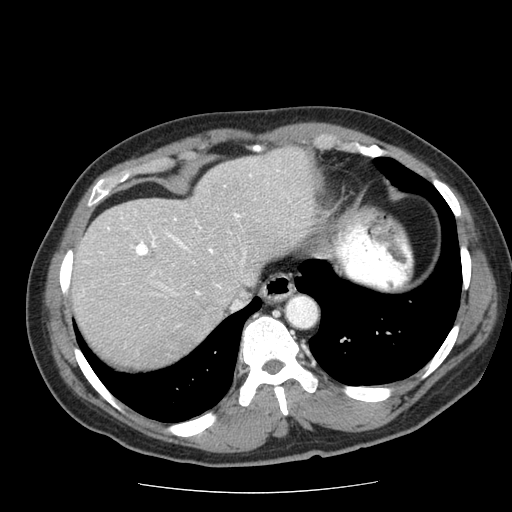
Contrast-enhanced abdominal CT (liver protocol), one axial slice. Position 54 of 85 along the scan axis. 120 kVp. Soft-tissue window (W 400 / L 40 HU). 512 × 512 image matrix. From the clinical record (not read from this slice): diagnosis: hepatocellular carcinoma (patient treated with transarterial chemoembolisation; whether this scan precedes or follows treatment is not stated here); TNM stage (as recorded): Stage-IIIA; Child-Pugh class: A; tumour differentiation: well differentiated; tumour nodularity: multinodular.
Outlined on this slice (semi-automatic segmentation, software-assisted and operator-edited):
- liver parenchyma outside the tumour (the mass and vessels are separate outlines, so this box may not span the whole liver): bounding box [x1, y1, x2, y2] px = [72, 146, 316, 368]
- liver vessels: [108, 170, 279, 295]